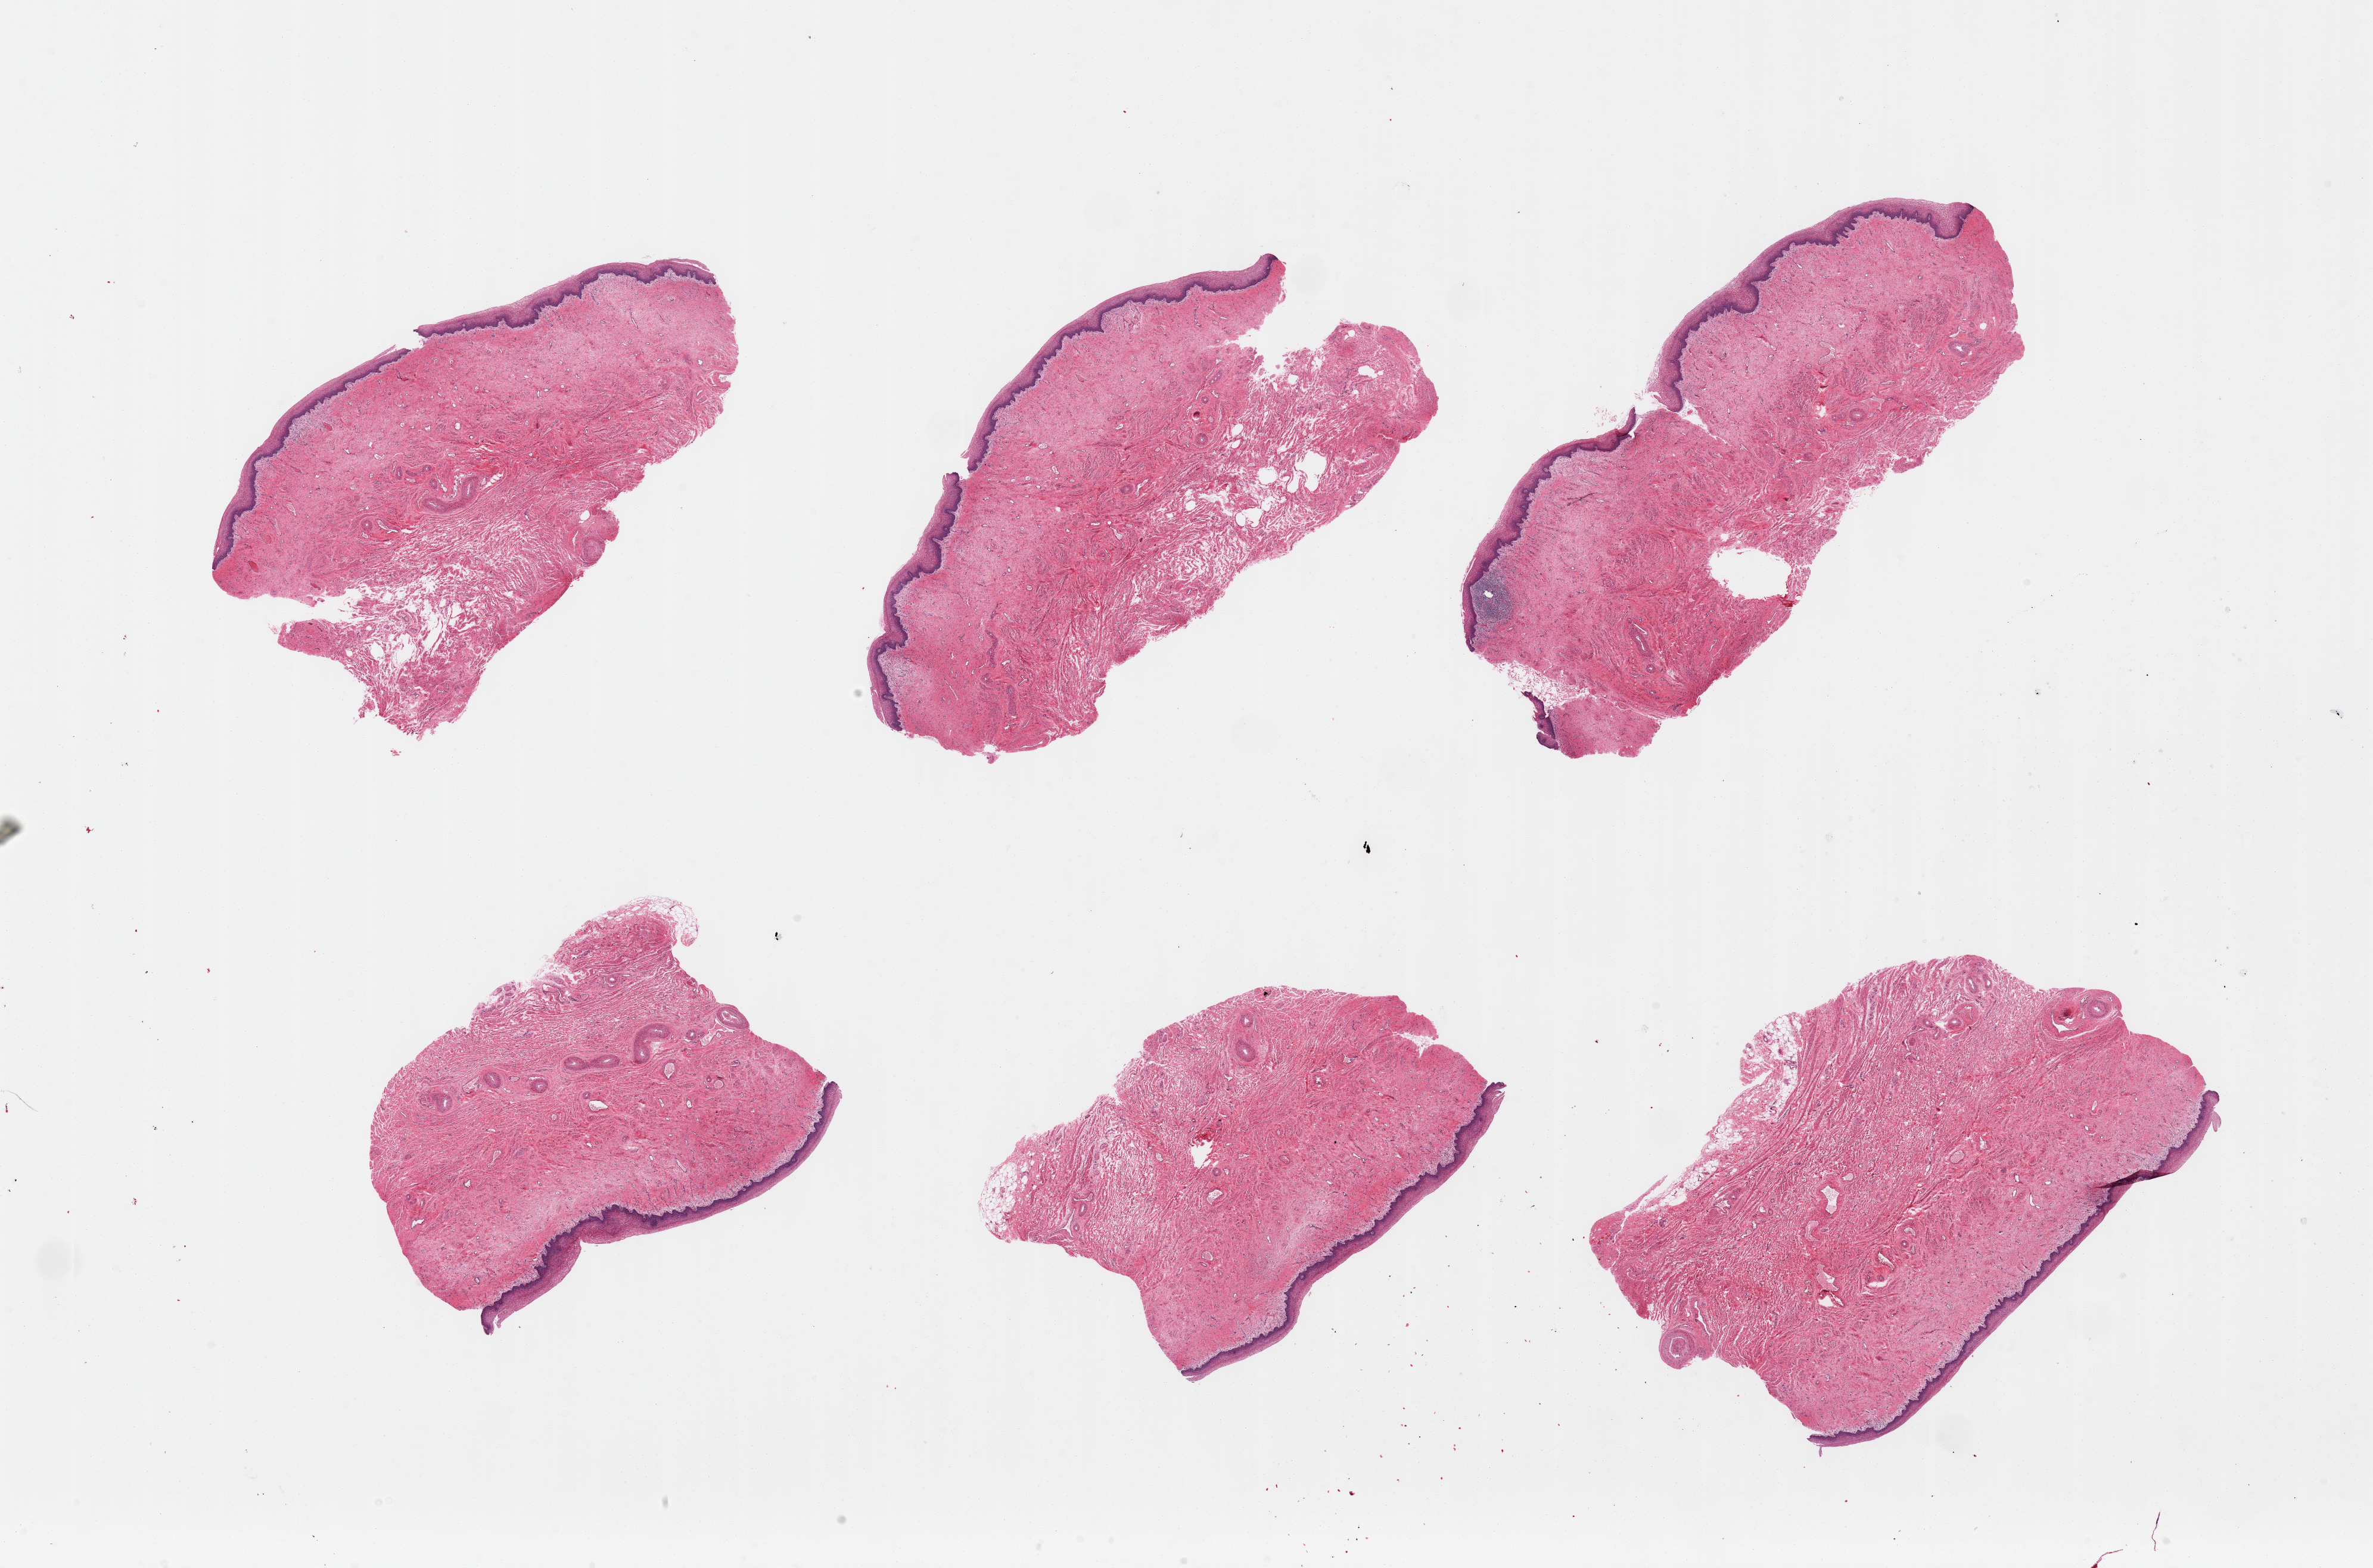
Digitized haematoxylin and eosin-stained section, brightfield, whole scanned area (about 31.5 x 20.8 mm, acquisition: 20x scan) shown as a low-resolution overview; PAXgene-fixed, paraffin-embedded tissue; sampled site (target tissue): vagina; tissue donor sample. Donor: female.
Reviewer comment on this tissue sample: 6 pieces.